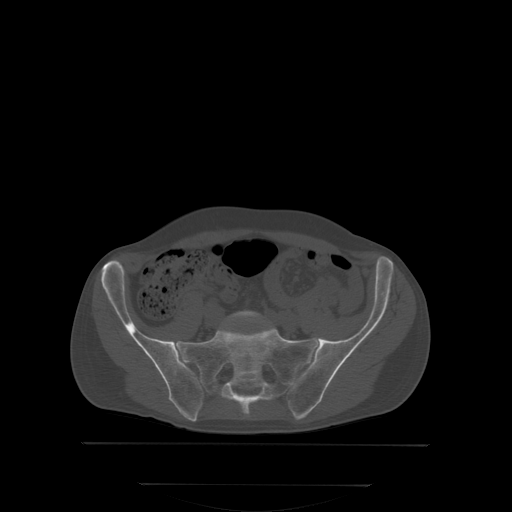
CT including the spine, one axial slice. Slice 82 of 350 in the series (ordered by position). Bone window (W 1800 / L 400 HU). 2.5 mm slice thickness. 512 × 512 image matrix, field of view 500 × 500 mm. Male patient, age 58 years. Case-level facts recorded for this patient, not image findings: primary cancer: prostate.
Annotated regions visible in this slice (semi-automatic segmentation, software-assisted and operator-edited):
- L5 vertebra: bounding box (x1, y1, x2, y2) in pixels: (217, 312, 269, 334)